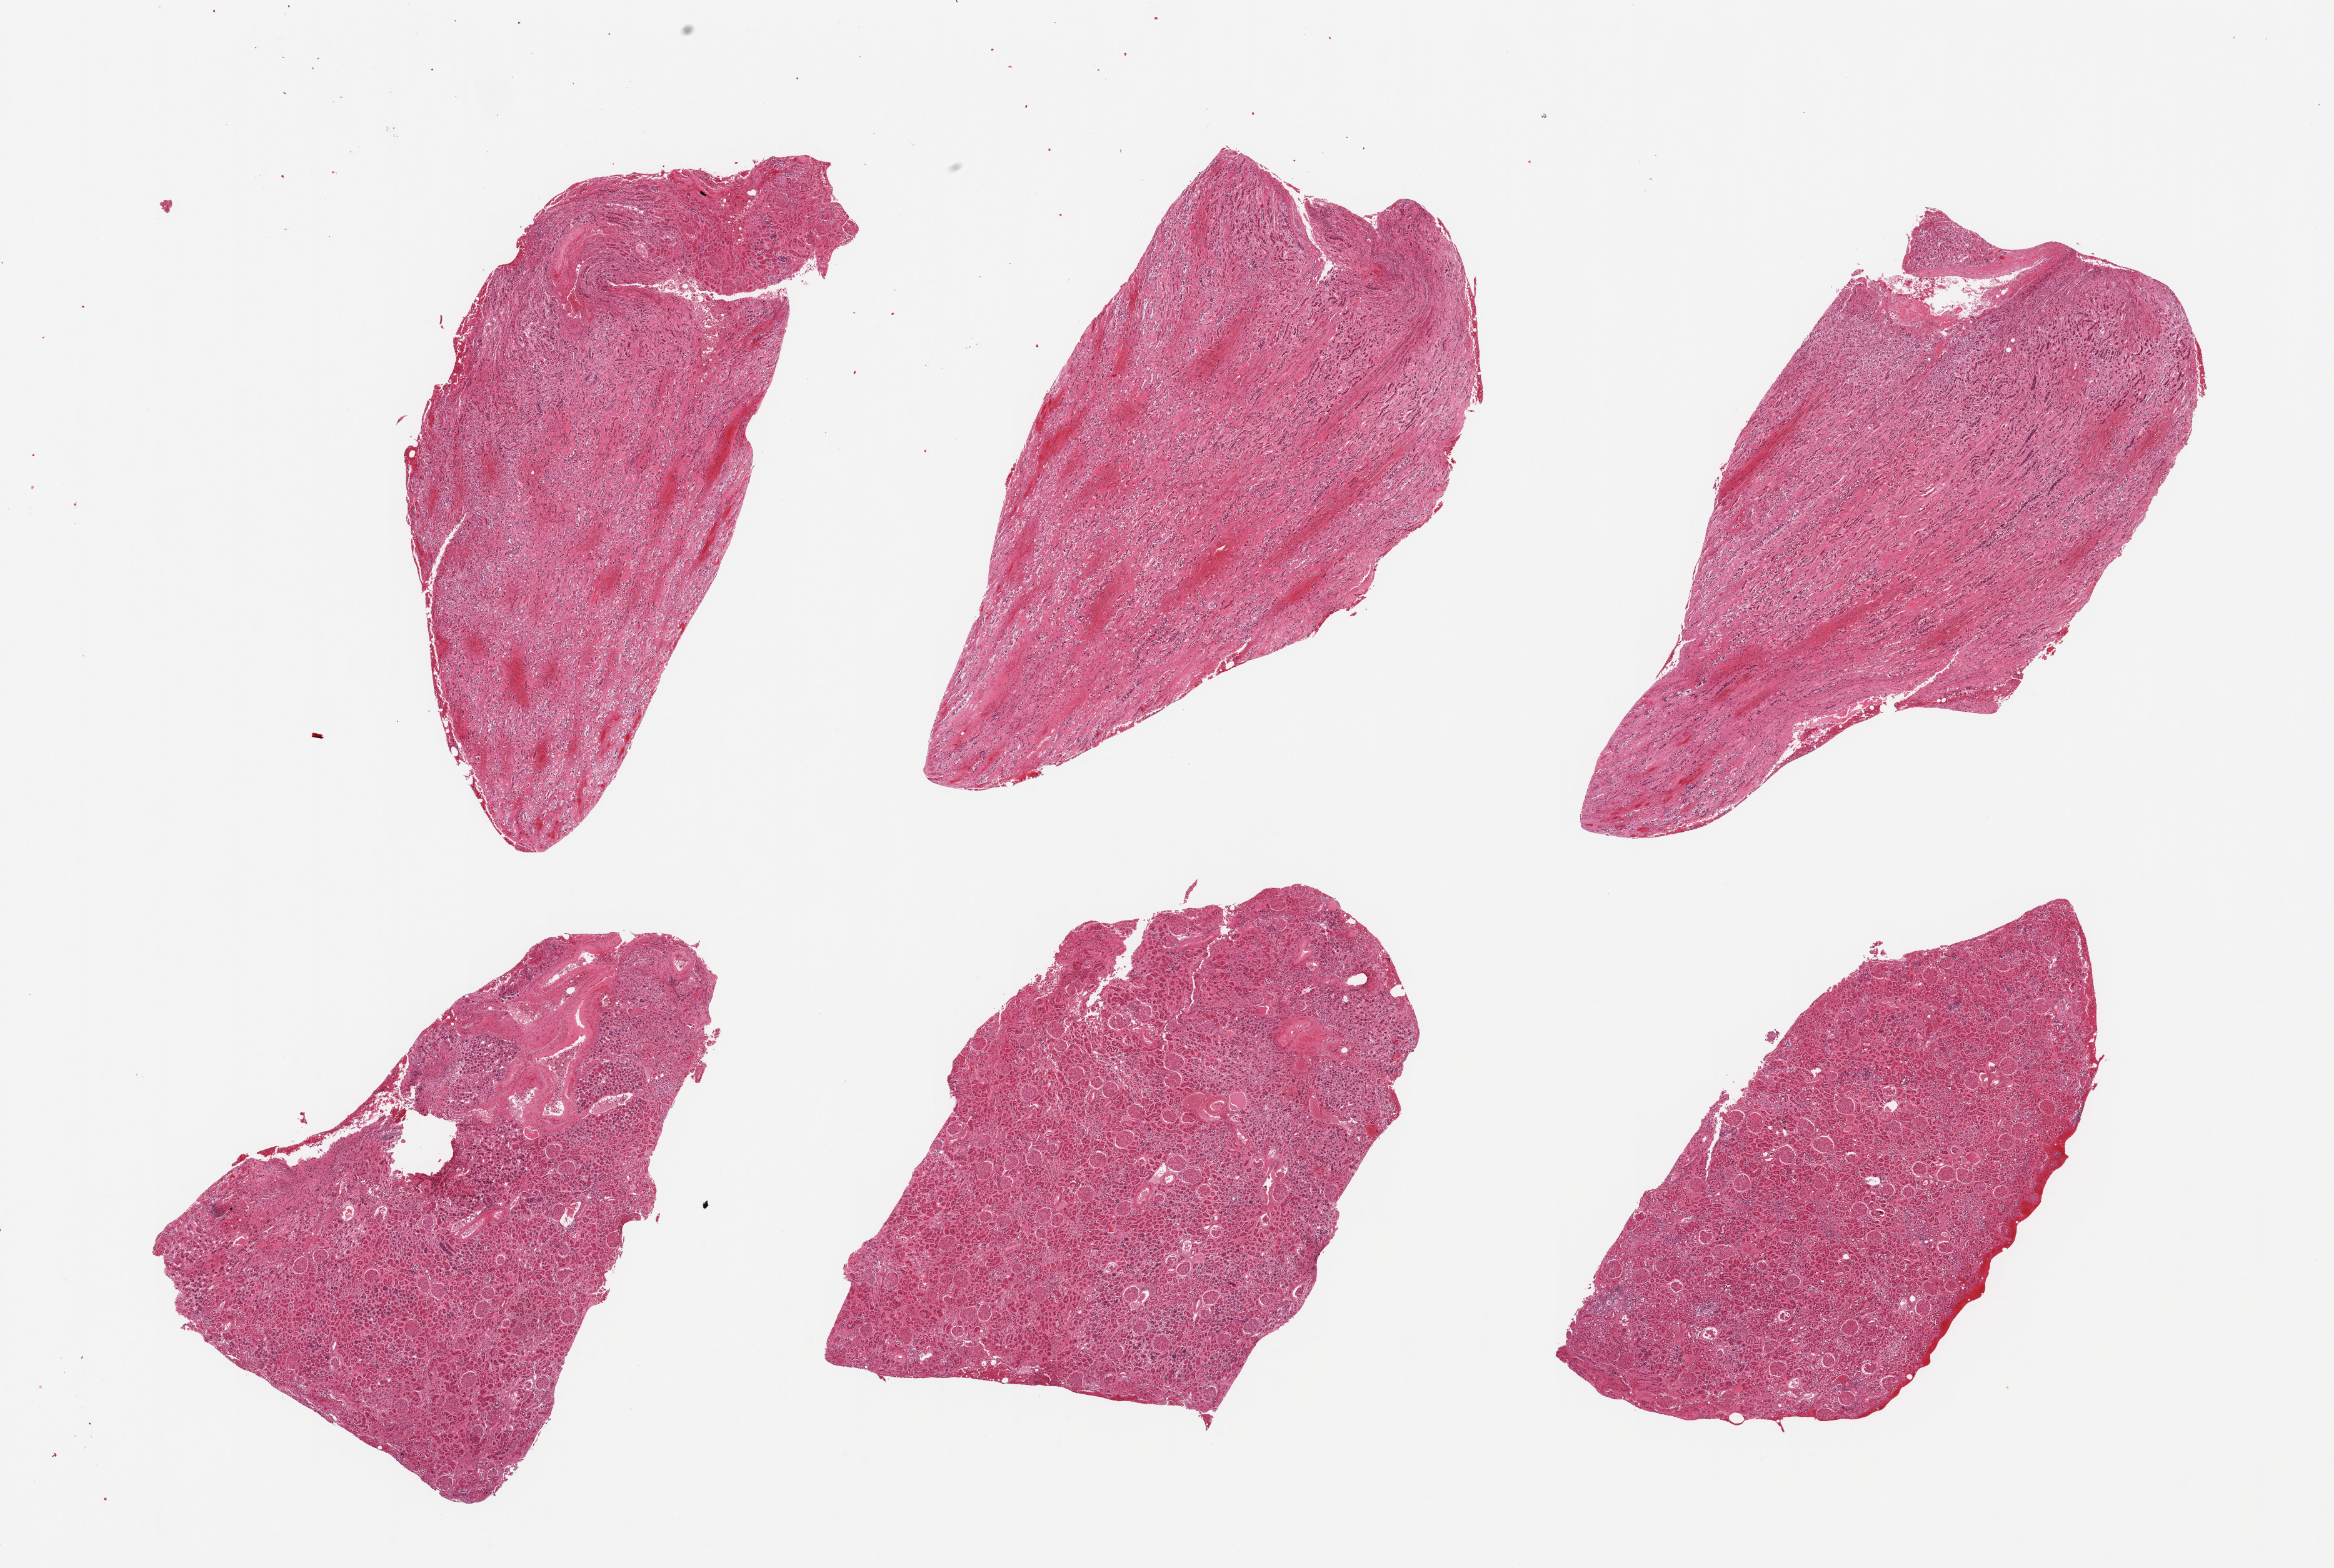
Haematoxylin and eosin whole-slide image — shown as a low-resolution overview of the whole scanned area (about 29.5 x 19.8 mm, acquisition: 20x scan). PAXgene-fixed paraffin-embedded (PFPE) section. Target tissue: renal cortex. Tissue donor sample. Donor sex: male.
Pathologist's review note for this sample: 6 pieces; some sclerotic glomeruli and vascular thickening, 3 are medulla (not target).